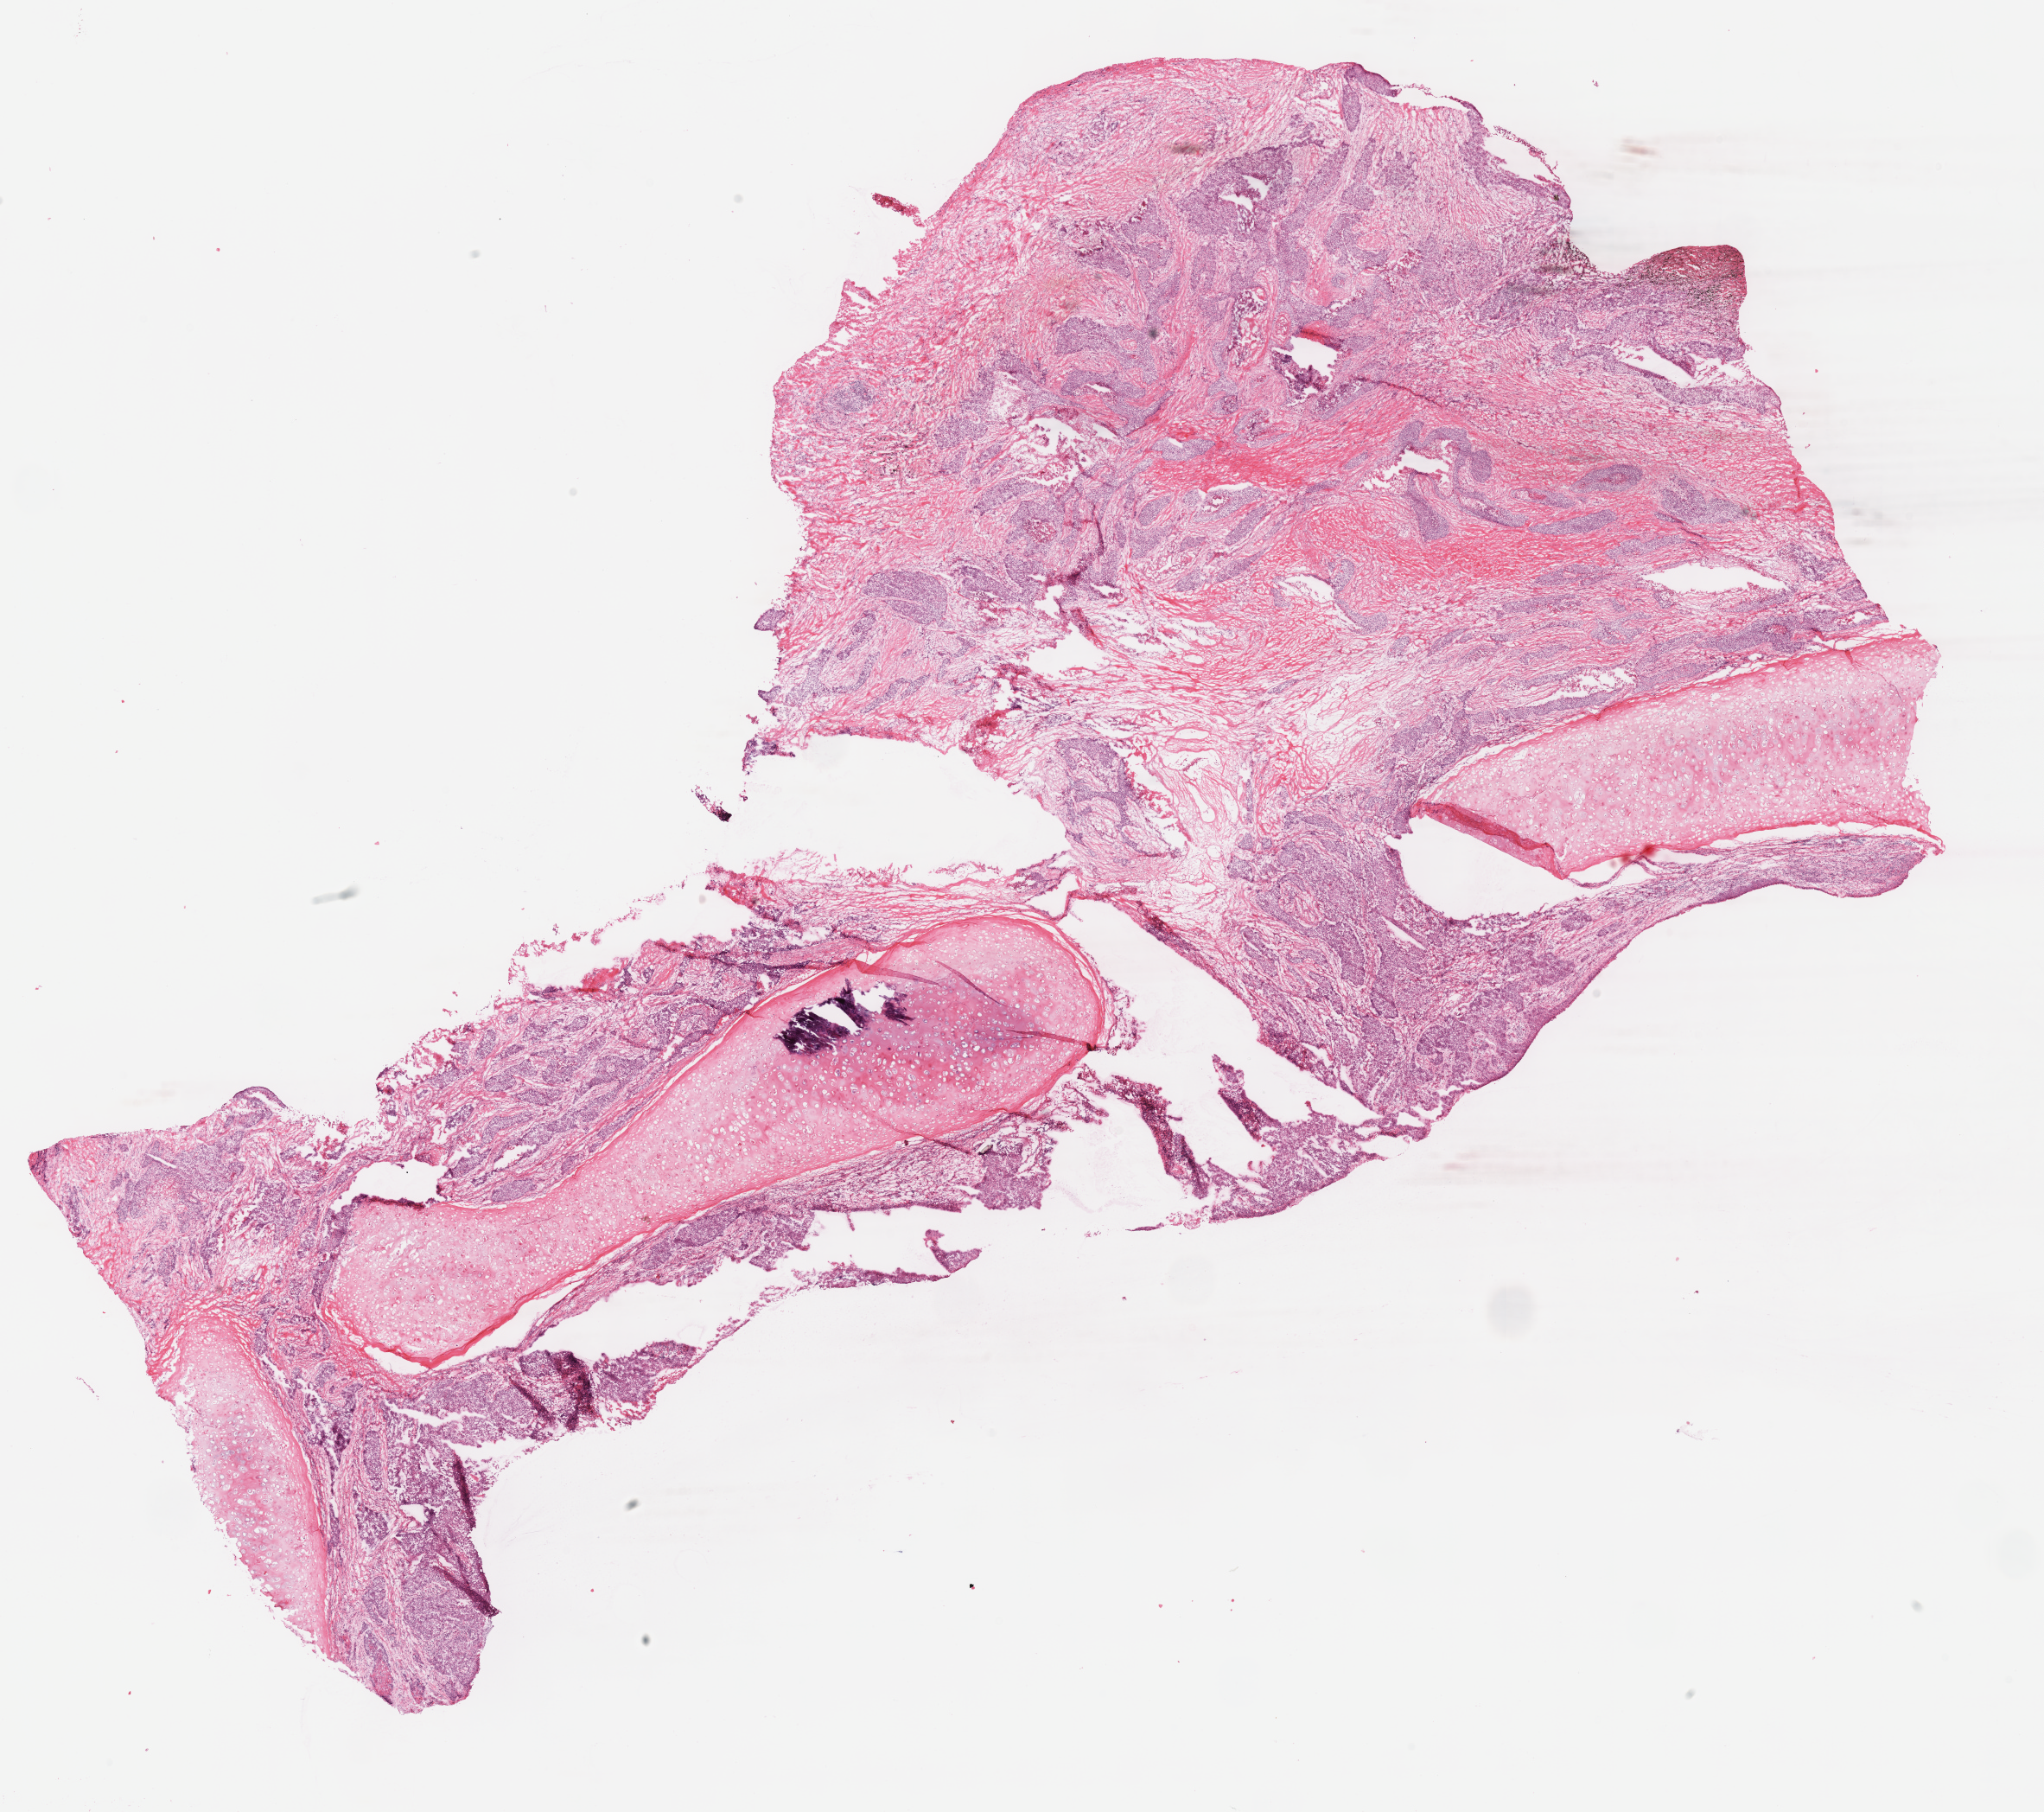
H&E-stained whole-slide image — whole scanned area (about 18.6 x 16.5 mm) shown as a low-resolution overview; frozen section; lung, primary tumour sample. Male patient; age at initial diagnosis 70 years. Pathologist review of this section (percent, as recorded): tumour cells 65%, tumour nuclei 80%, normal cells 0%, stromal cells 30%, necrosis 5%.
- laterality: right
- AJCC pathologic stage: IIA (7th edition)
- histologic diagnosis: Squamous cell carcinoma, NOS (middle lobe, lung)